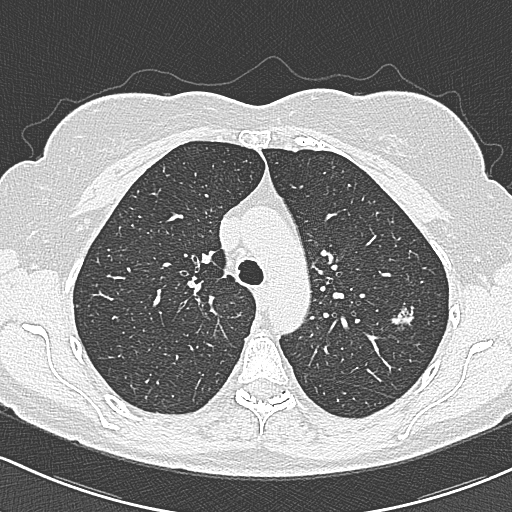
Axial slice from a low-dose chest CT screening exam. Baseline screening round. Lung window (W 1500 / L -600 HU). 1 mm slice thickness. Lung (sharp) reconstruction kernel (B80f). 120 kVp. Slice 88 of 312 in the series. 512 × 512 image matrix, field of view 318 × 318 mm. Female participant, aged 65 years at enrolment. Current smoker at enrolment.
Lesion marked by an expert reader, box from (x=383, y=299) to (x=424, y=337) px. The screening reader recorded 3 non-calcified nodules or masses ≥4 mm on this exam (left upper lobe, left upper lobe, right upper lobe); which of them this box marks is not recorded. Official screen result: positive, change unspecified: nodule(s) >= 4 mm or enlarging nodule(s), mass(es), or other non-specific abnormalities suspicious for lung cancer. Later outcome: lung cancer diagnosed 390 days after this screen — bronchiolo-alveolar carcinoma, non-mucinous, left upper lobe, stage IA (AJCC 6th edition), 10 mm at pathology.